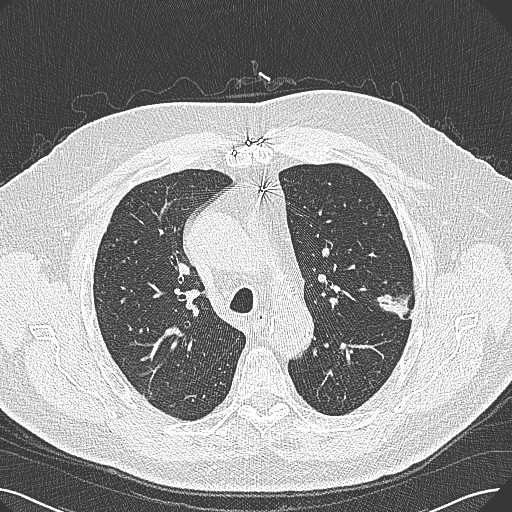
Axial slice from a low-dose chest CT screening exam, baseline screening round, lung window (W 1500 / L -600 HU), lung (sharp) reconstruction kernel (B80f). Male participant, aged 74 years at enrolment. Former smoker at enrolment.
Expert-annotated lung lesion, bounding box <368,273,426,323> (left, top, right, bottom; pixels). Reader record for this screening exam (exam-level; its link to the box is not recorded): non-calcified nodule or mass ≥4 mm, left upper lobe, 15 × 10 mm, poorly defined margins, soft tissue attenuation.